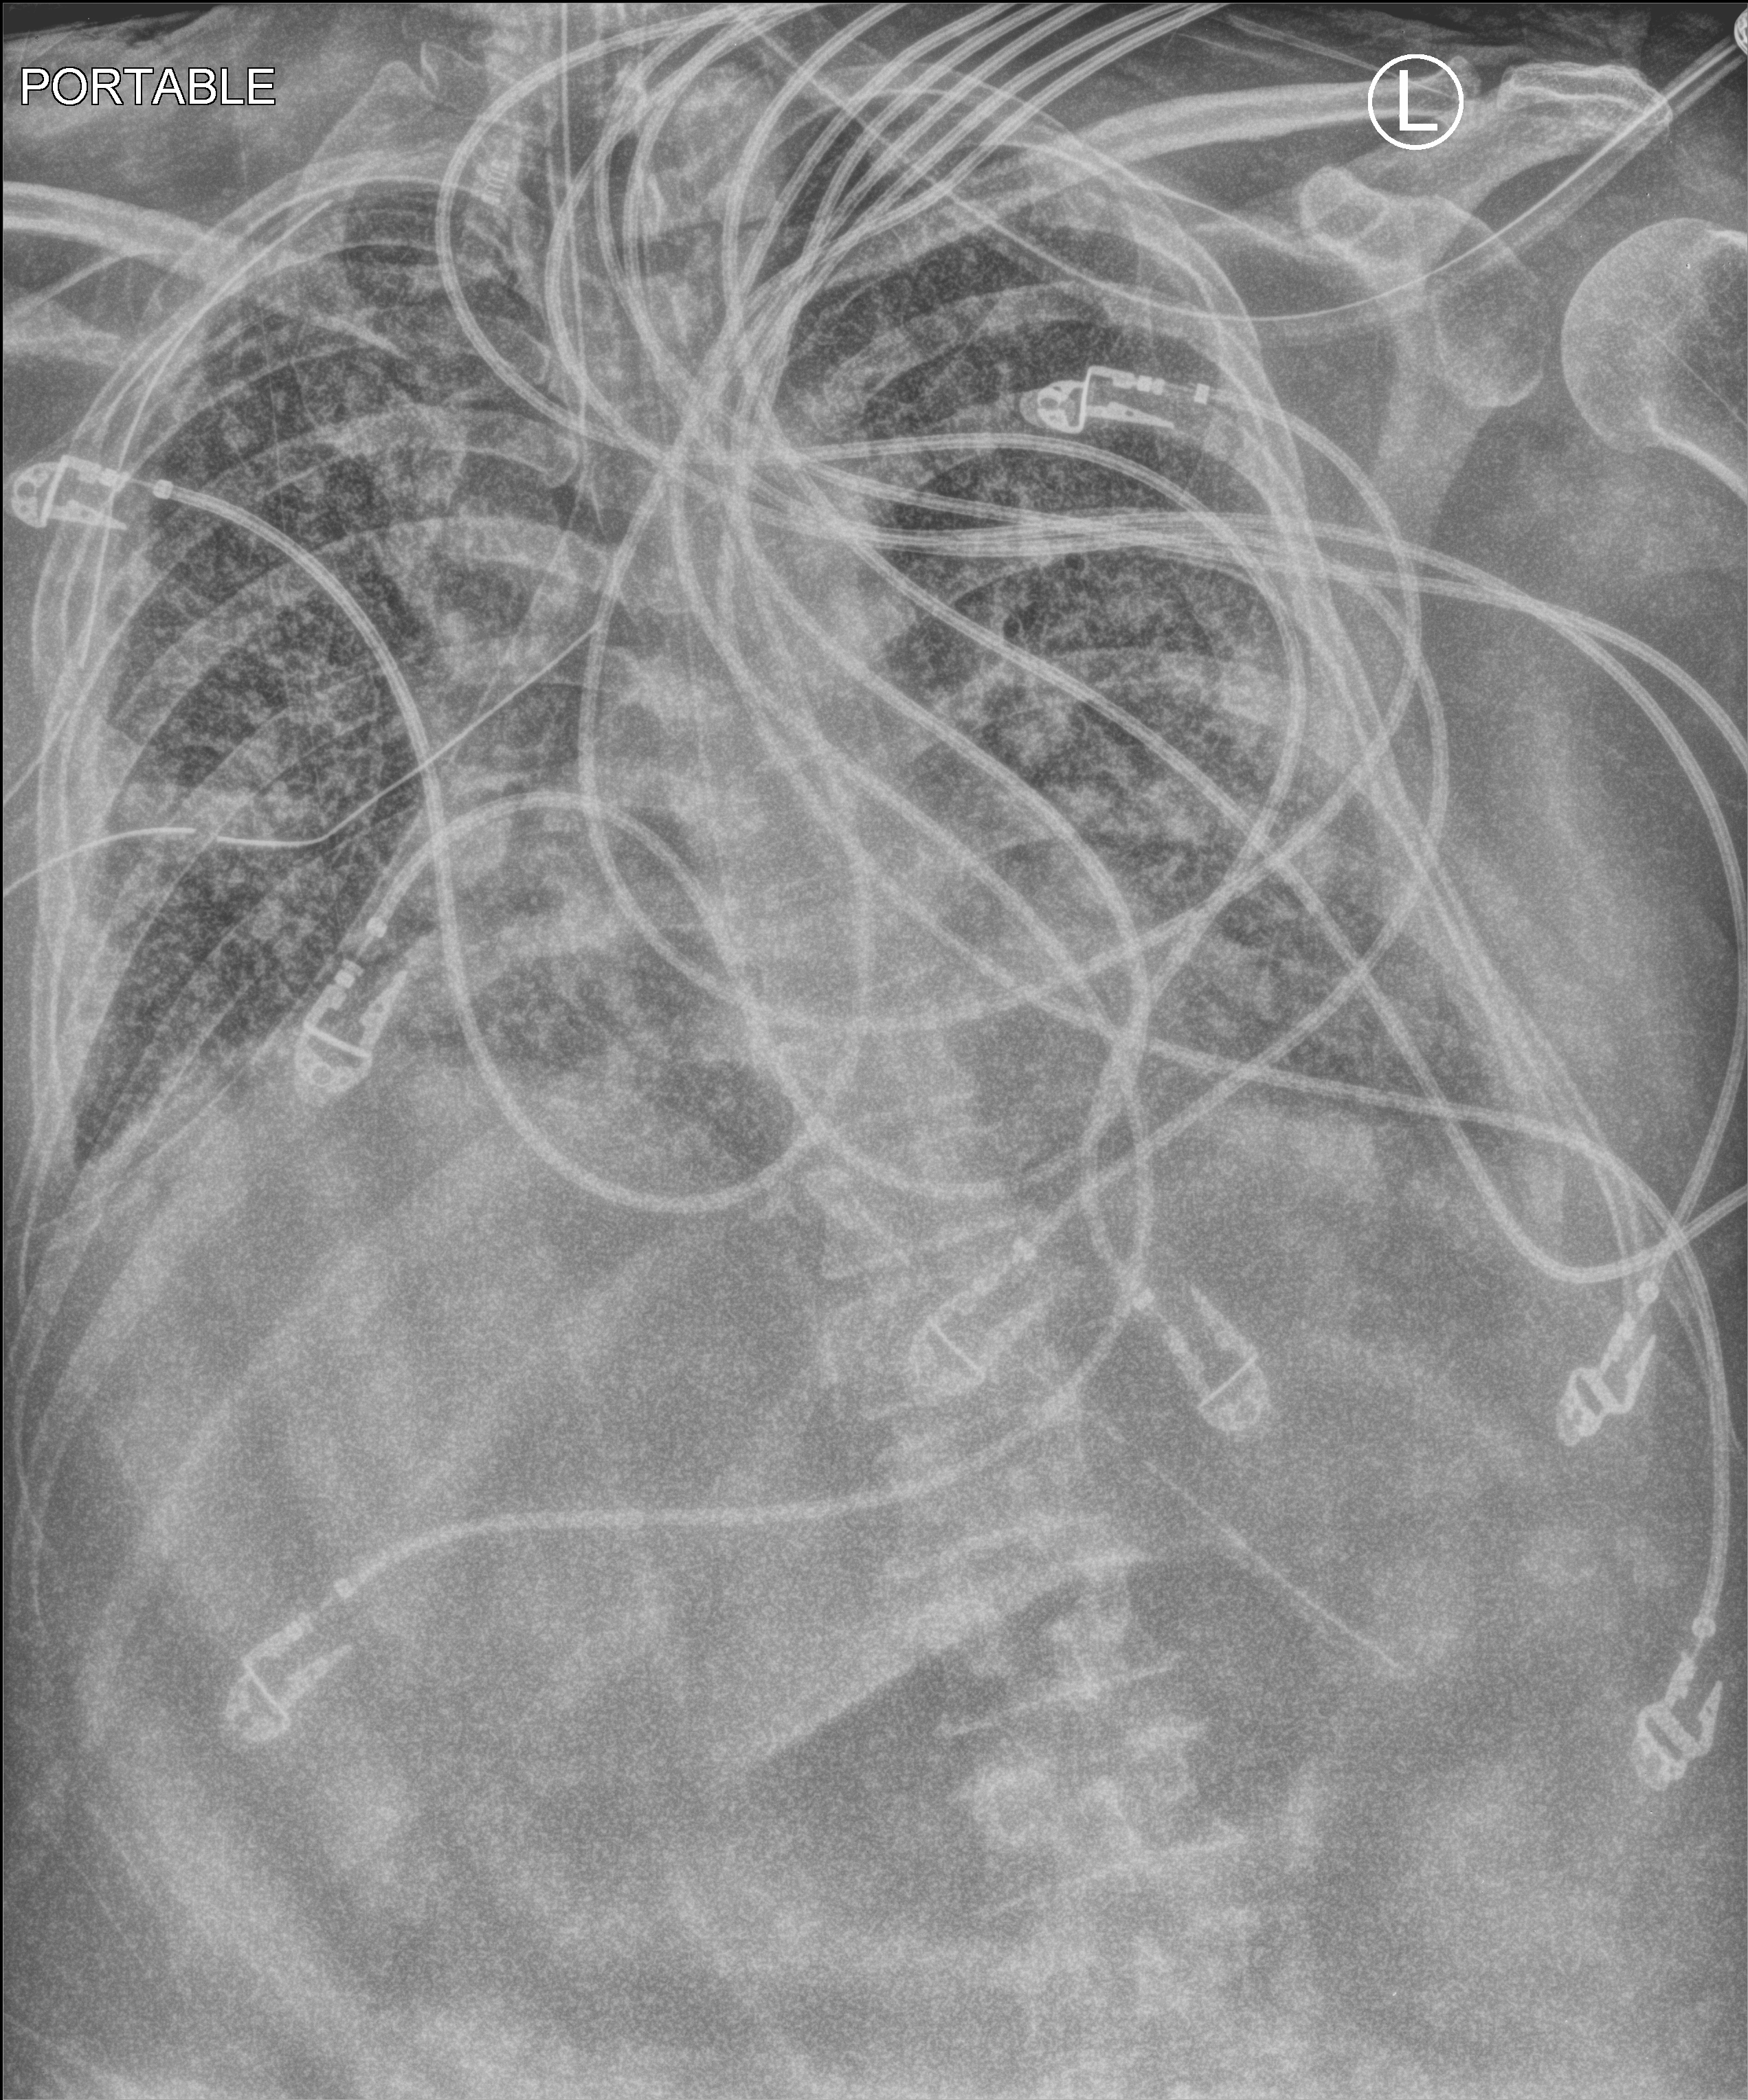
Portable chest radiograph, anteroposterior (AP) projection. Adult patient hospitalised with COVID-19, age 18–59 years.
From the hospital-stay record, not from the radiograph (when in the stay this image was taken is not recorded): admitted to intensive care during this hospital stay: yes; smoking status (admission record): never.